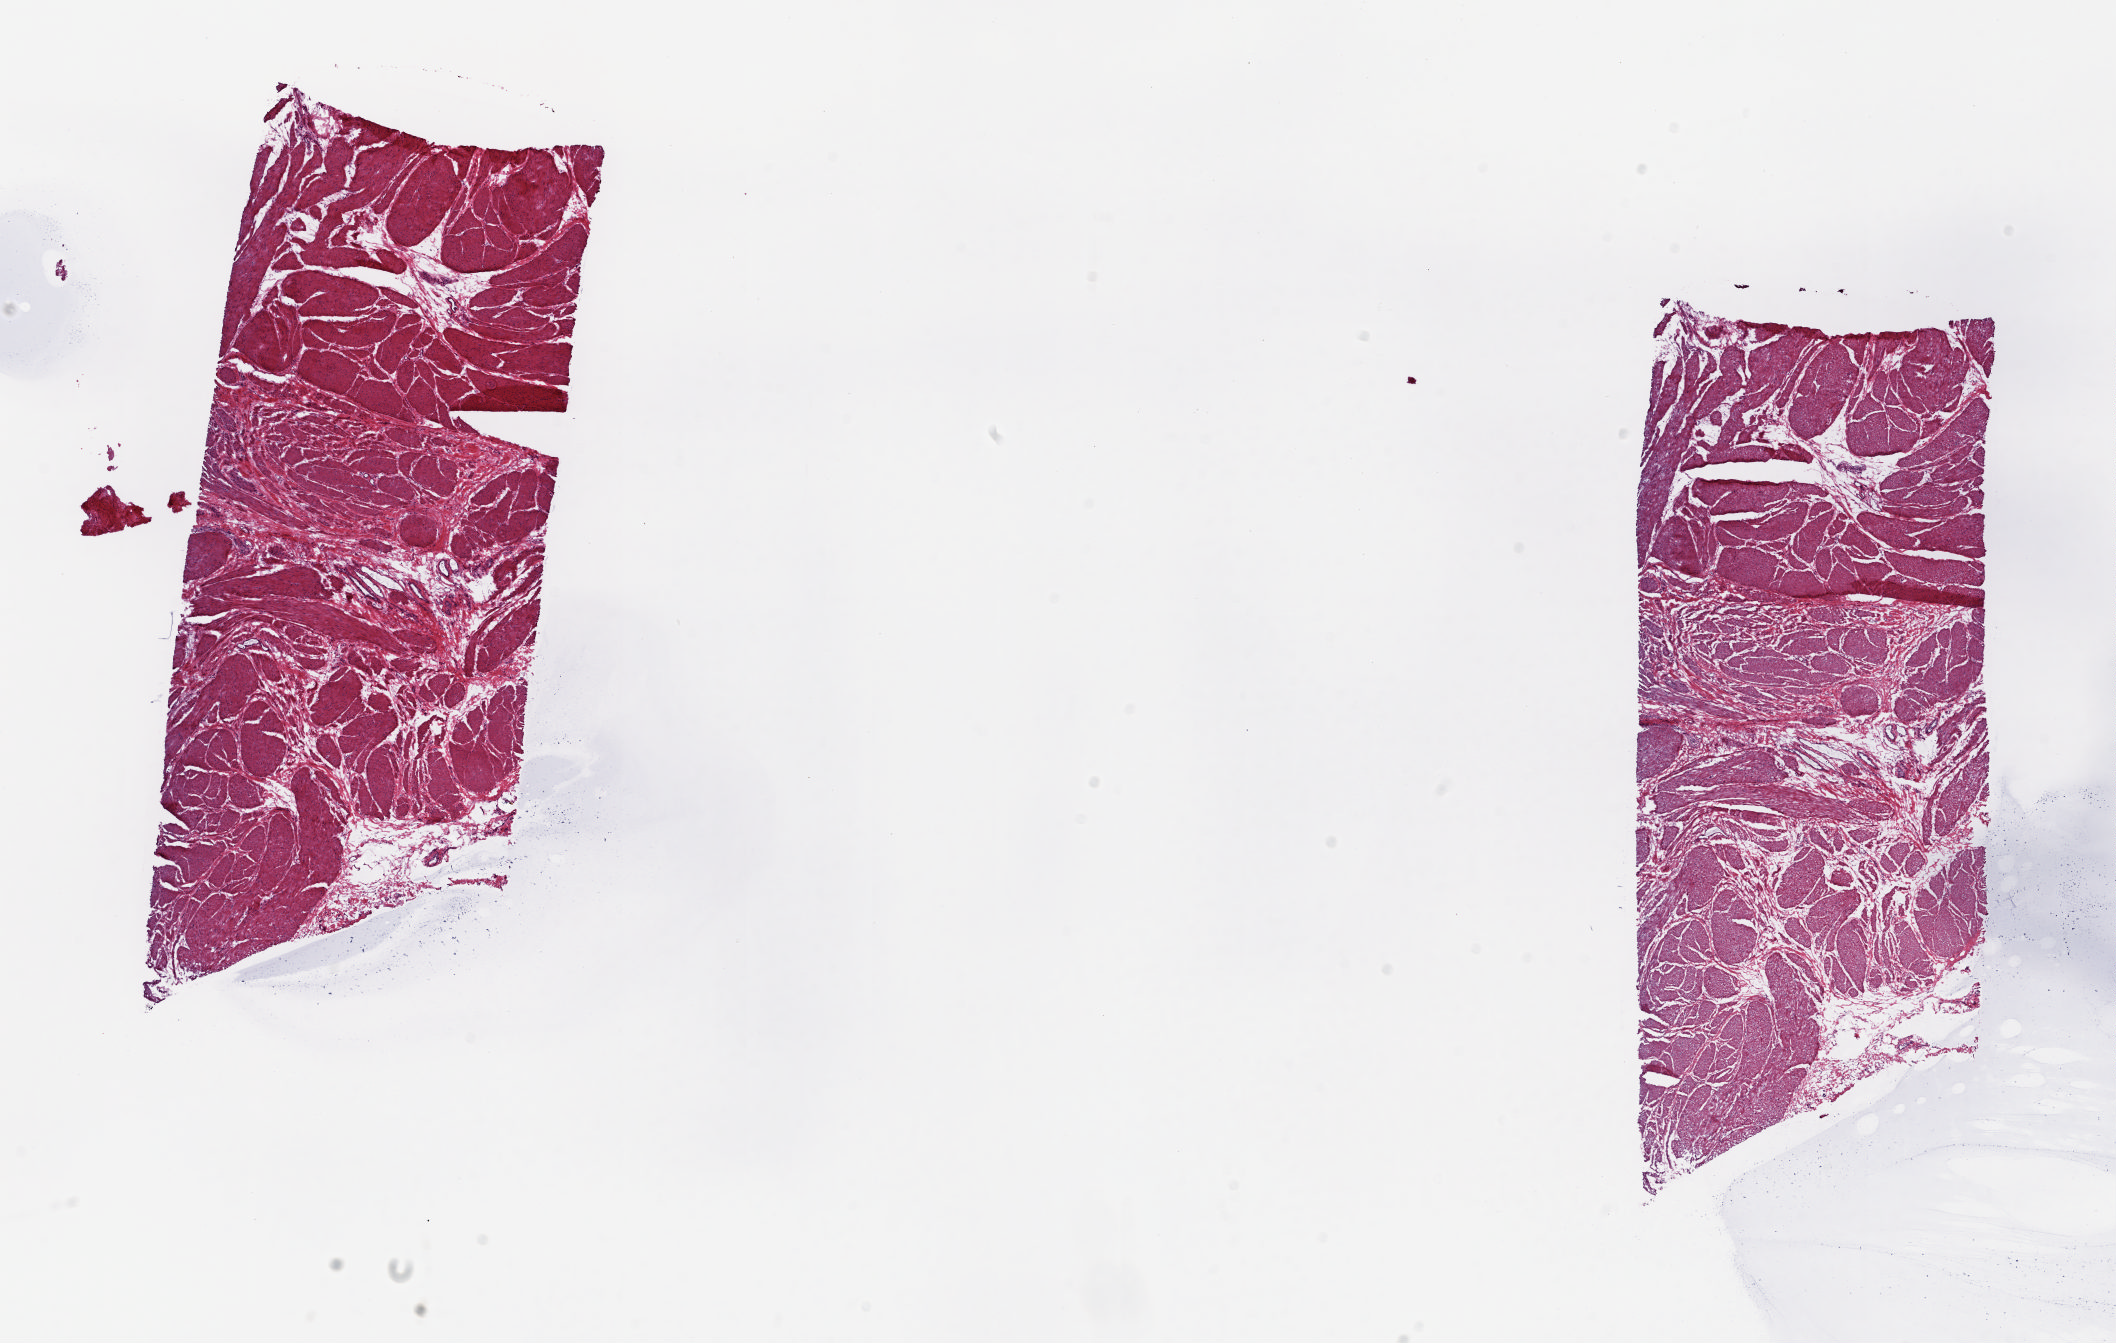
H&E-stained whole-slide image — shown as a low-resolution overview of the whole scanned area (about 16.8 x 10.7 mm); frozen section from the top of the tissue portion; sample: solid tissue normal (non-tumour tissue), bladder. Patient: male, age at initial diagnosis 73 years. Pathologist review of this section (percent, as recorded): tumour cells 0%, tumour nuclei 0%, normal cells 100%, stromal cells 0%, necrosis 0%. Inflammatory infiltration, as recorded: lymphocyte infiltration 0%, monocyte infiltration 0%, neutrophil infiltration 0%.
This section: solid tissue normal (non-tumour) sample from the same patient. Patient diagnosis: Transitional cell carcinoma (trigone of bladder).